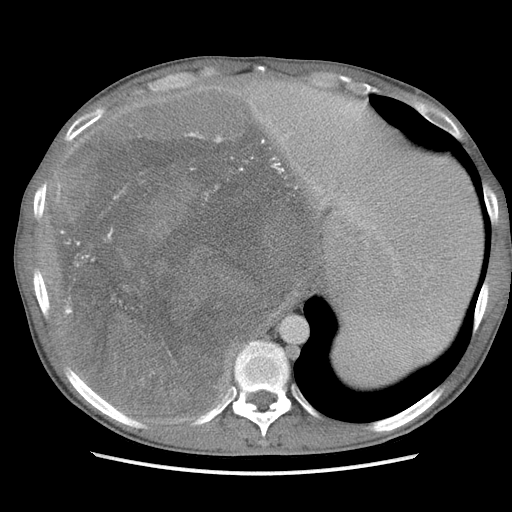
Contrast-enhanced abdominal CT, one axial slice. Position 86 of 115 along the scan axis. Soft-tissue window (W 400 / L 40 HU). 512 × 512 image matrix, field of view 360 × 360 mm. Male patient. Case-level facts recorded for this patient, not image findings: diagnosis: adrenocortical carcinoma; tumour side: right adrenal; Ki-67 index: 13 %; stage (as recorded): 3.
Annotated regions visible in this slice (semi-automatic segmentation, software-assisted and operator-edited):
- mass: bounding box [x1, y1, x2, y2] px = [58, 92, 317, 411]